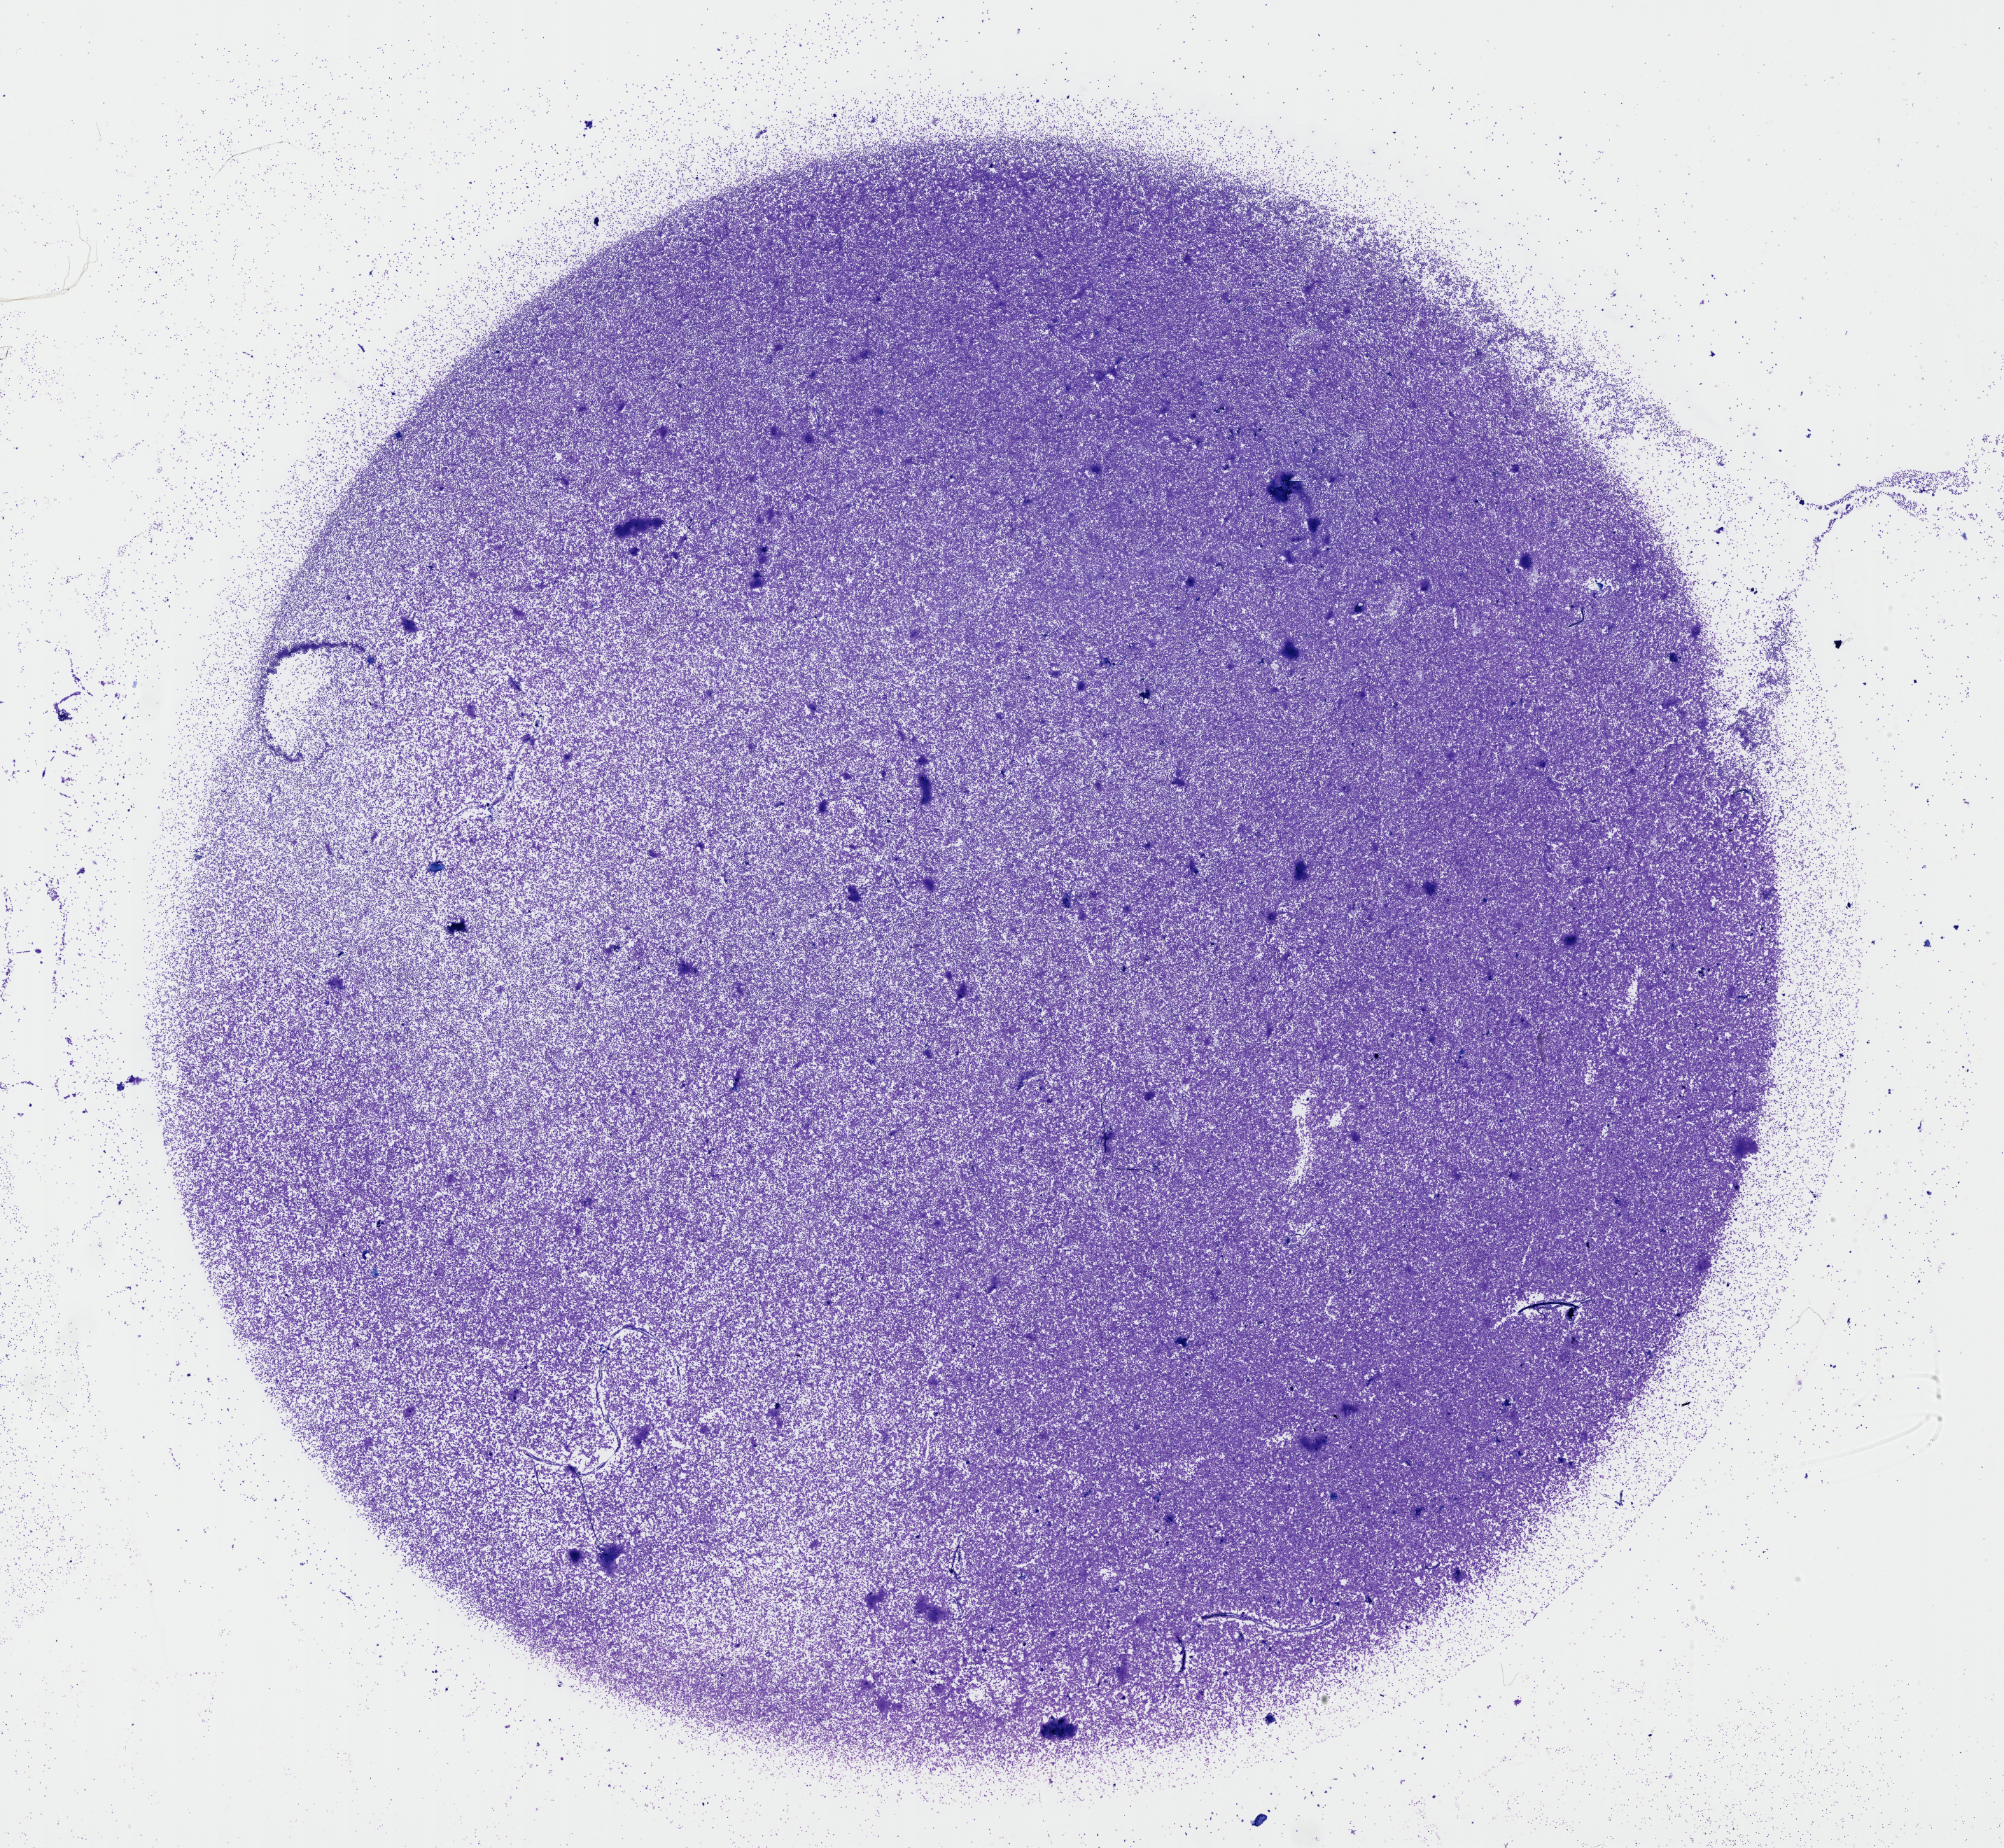
Digitized H&E tissue section (whole slide) — low-resolution overview of the scanned area, about 23.1 x 21.3 mm; bone marrow (leukaemic) sample. Female, 58 y/o. Blasts: 80%.
Diagnosis: Acute Myeloid Leukemia. FAB classification: M4. WHO classification: Acute myelomonocytic leukemia.